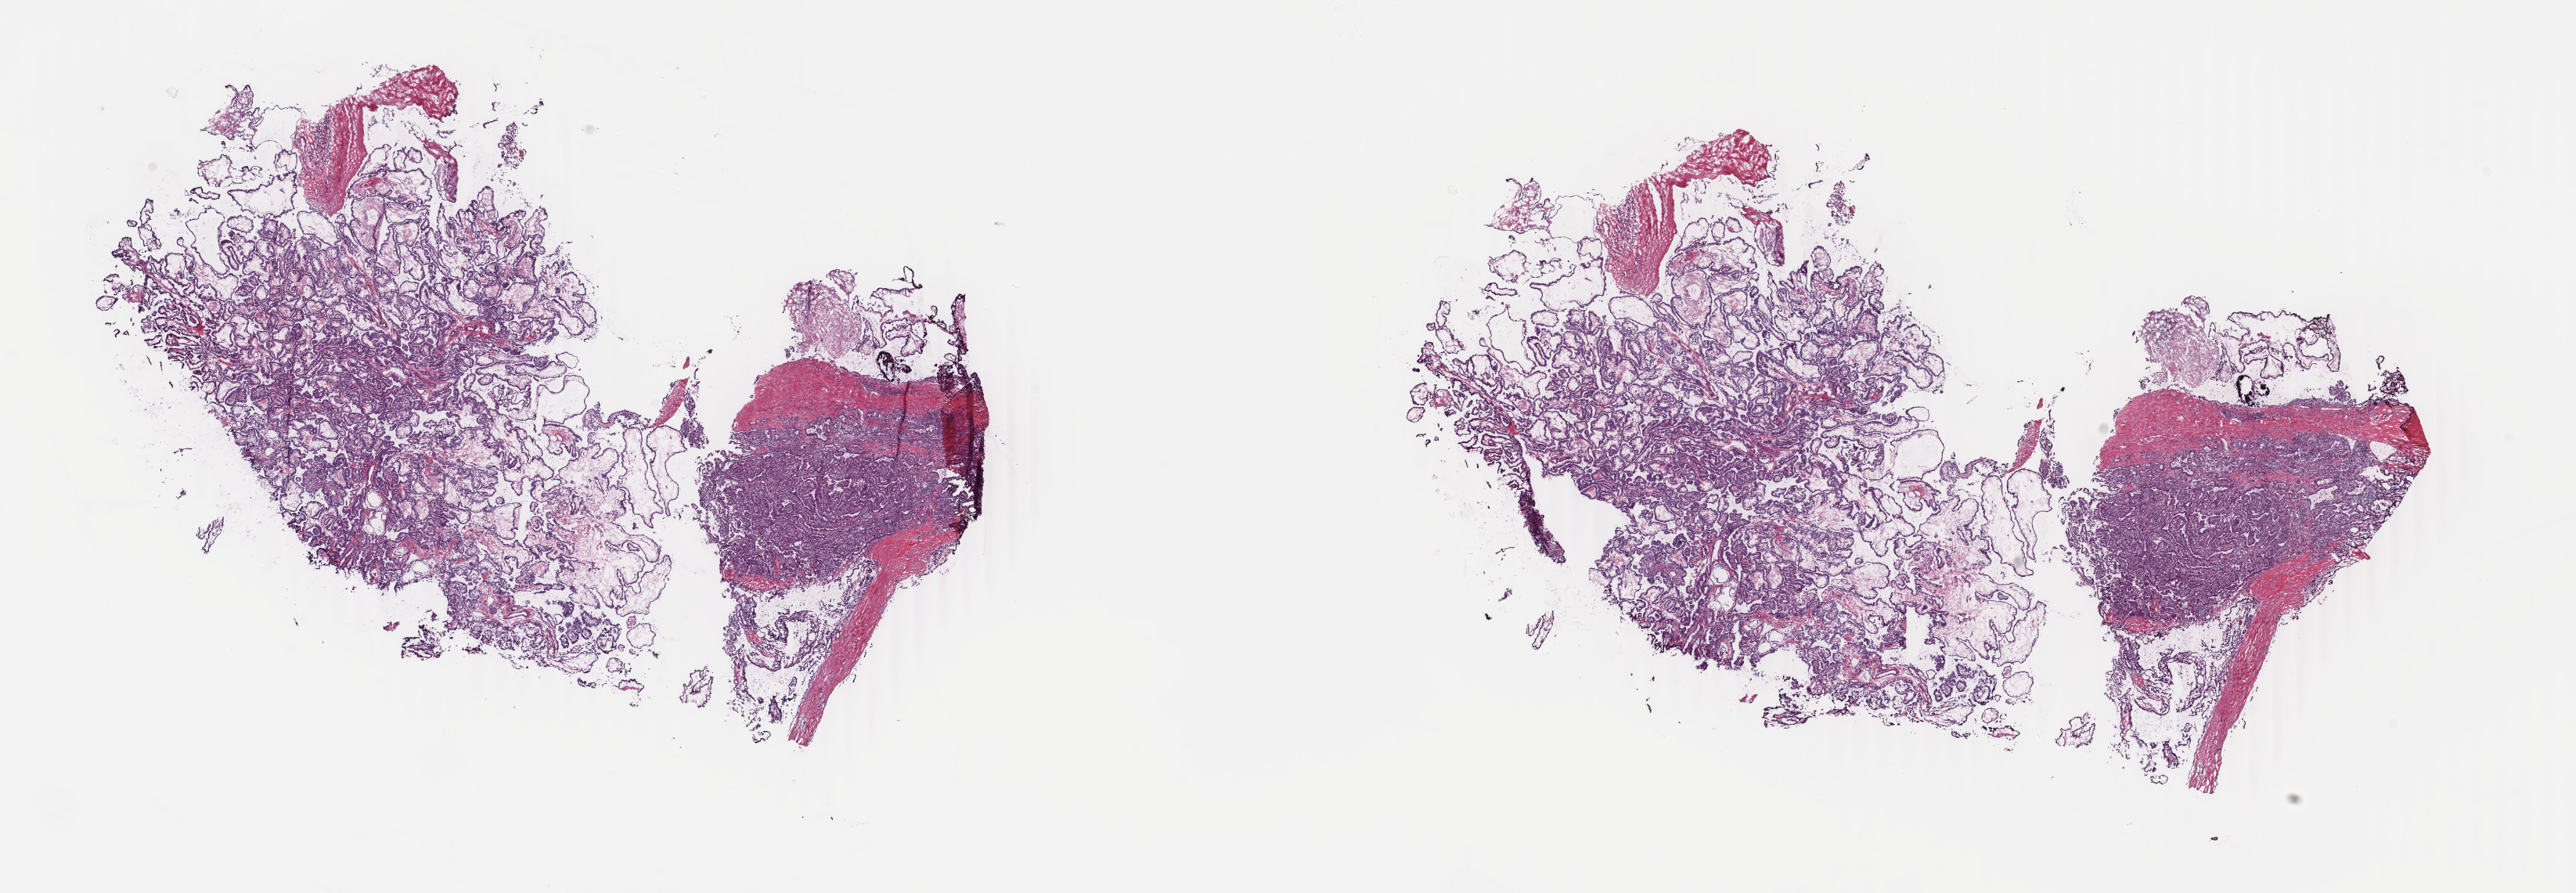
Digitized Hematoxylin and eosin (H&E) stained tissue section (whole slide), shown as a low-resolution overview of the whole scanned area (about 26.2 x 9.1 mm, acquisition: 40x scan), frozen section from the top of the tissue portion, thyroid, primary tumour sample. Female patient; age at initial diagnosis 39 years.
Histologic diagnosis: Papillary adenocarcinoma, NOS (thyroid gland).